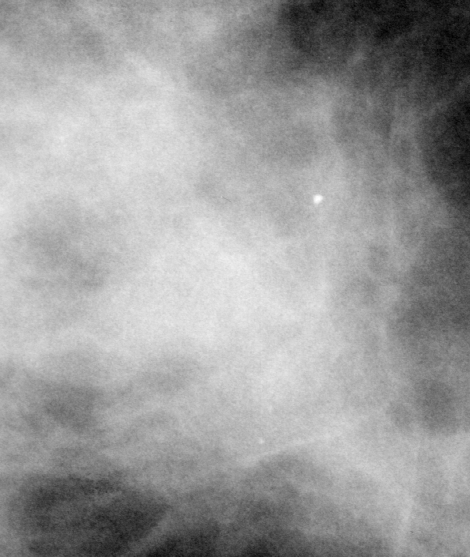
Cropped region of a digitized screen-film mammogram centred on a radiologist-marked abnormality, left breast, CC view, BI-RADS breast density category 2 (scale 1–4).
Mass, shape irregular, margins ill defined; BI-RADS assessment category 5; pathology result (as recorded, not read from the image): malignant.